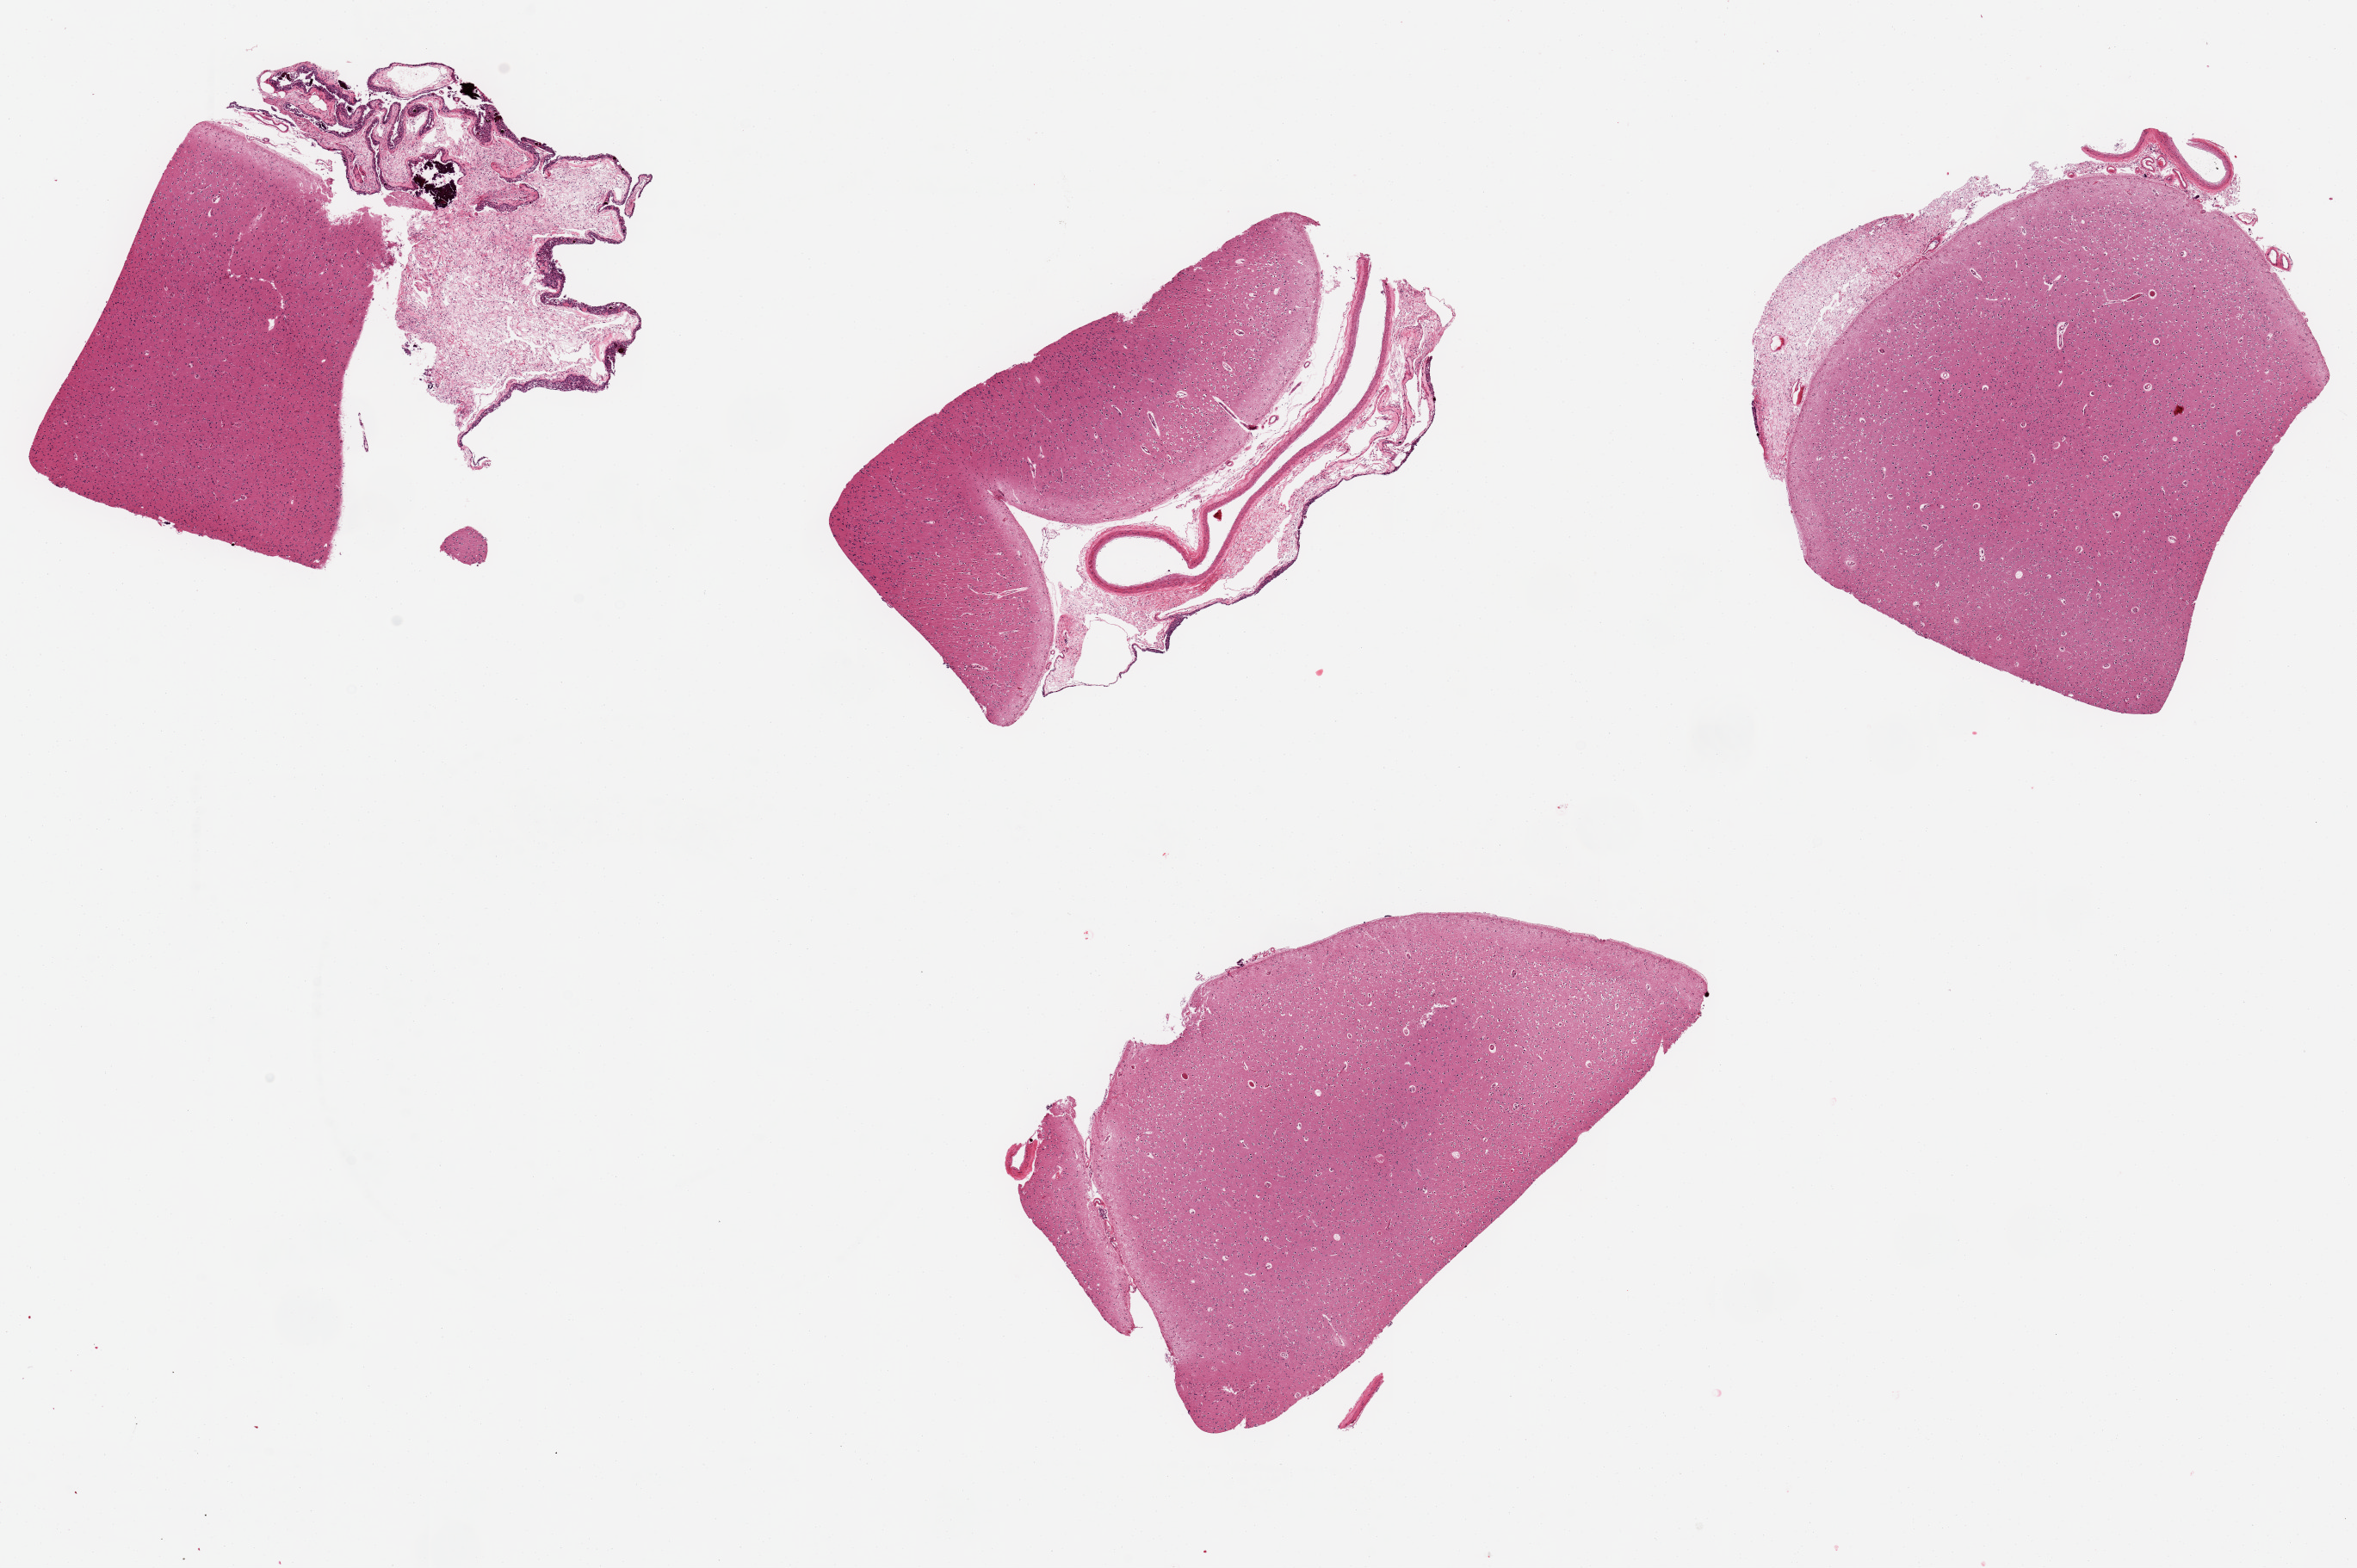
H&E whole-slide image, a low-resolution overview of the entire scanned area, about 21.7 x 14.4 mm (acquisition: 20x scan). PAXgene-fixed paraffin-embedded (PFPE) section. Sampled site (target tissue): cerebral cortex. Tissue donor sample.
* review note (as recorded): 4 ~ 5x3mm pieces, fragments of adherent dura/pia mater are present